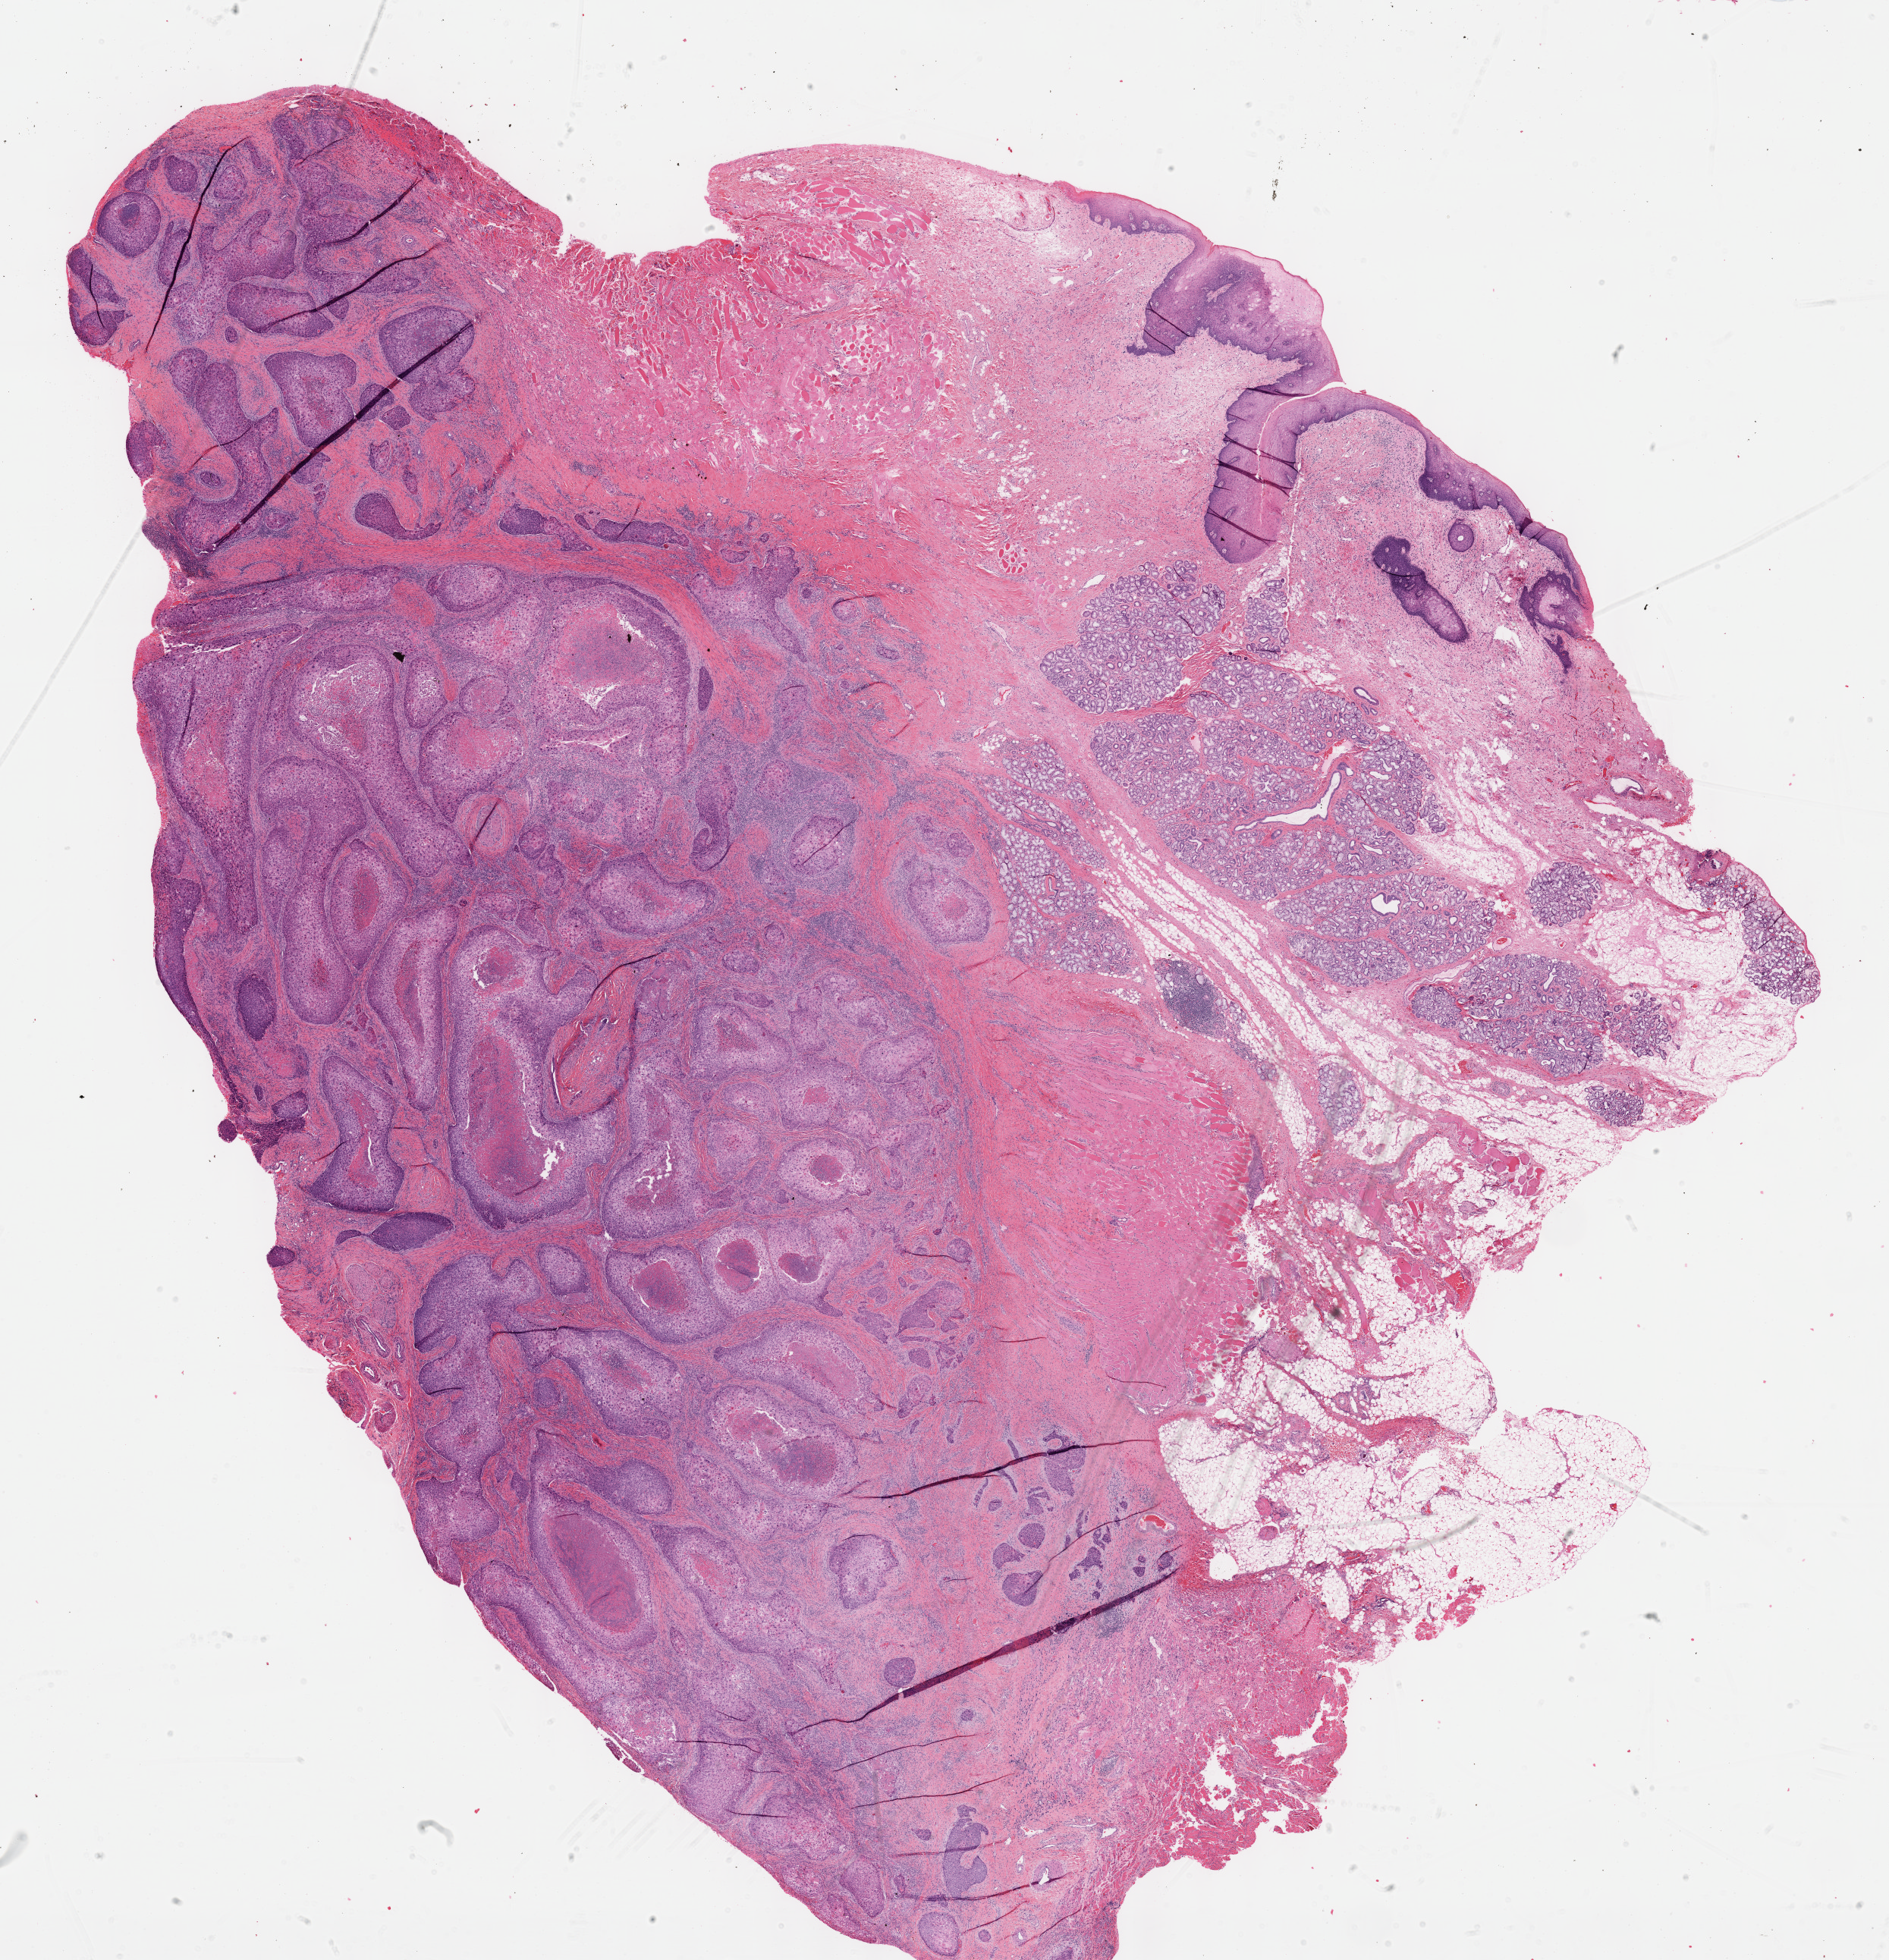
H&E whole-slide image, a low-resolution overview of the entire scanned area, about 20.1 x 20.9 mm (from a 40x scan), formalin-fixed paraffin-embedded (FFPE) diagnostic section, head and neck, primary tumour sample. Patient: female, age at initial diagnosis 64 years. Histologic grade: G3 (poorly differentiated).
Pathologic diagnosis: Squamous cell carcinoma, NOS (overlapping lesion of lip, oral cavity and pharynx). AJCC pathologic stage: IVA (7th edition). TNM: T4a N2.